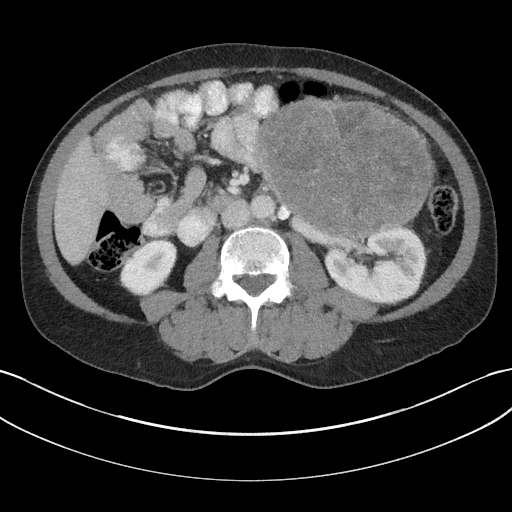
Contrast-enhanced abdominal CT, one axial slice; slice 83 of 147 in the series (ordered by position); reconstruction kernel I31f/3; 100 kVp; intravenous contrast given; soft-tissue window (W 400 / L 40 HU); 3 mm slice thickness; 512 × 512 image matrix, field of view 384 × 384 mm. Male patient, age 58 years. From the clinical record (not read from this slice): diagnosis: adrenocortical carcinoma; tumour side: left adrenal.
Structures marked on this image (semi-automatic segmentation, software-assisted and operator-edited):
- mass: bounding box [x1, y1, x2, y2] px = [262, 97, 429, 233]